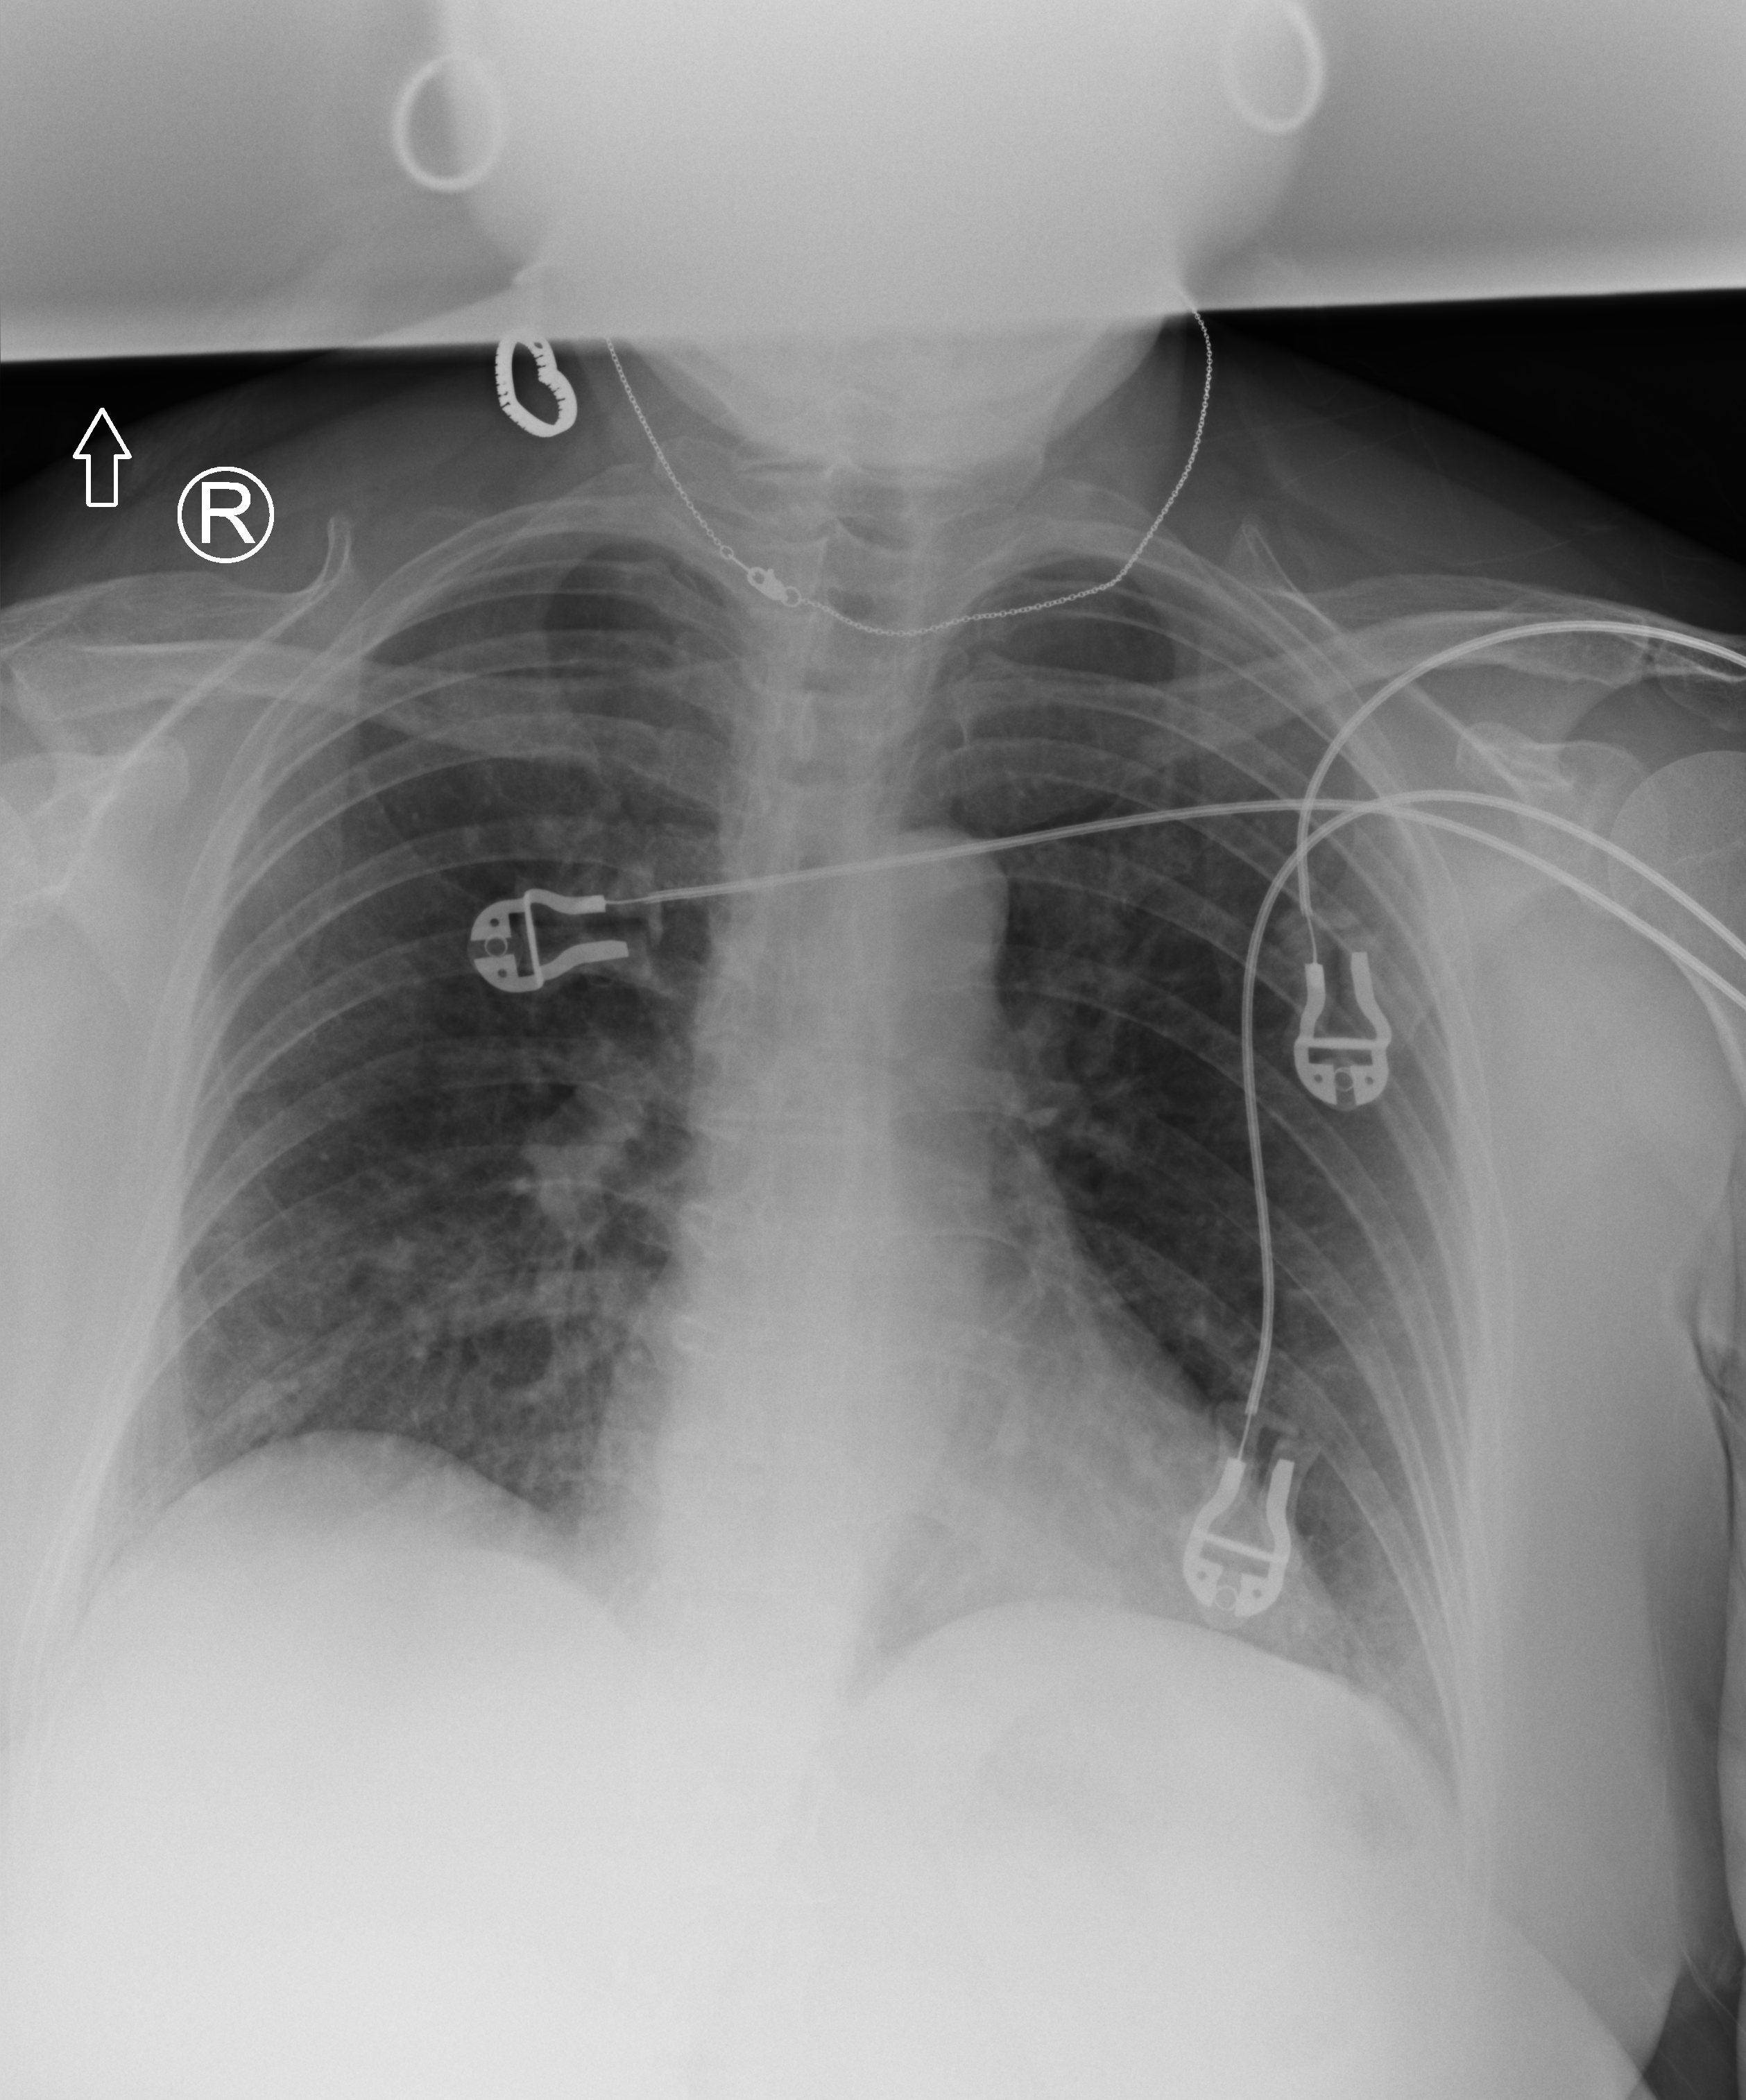
Chest X-ray (portable); anteroposterior (AP) projection. Patient hospitalised with COVID-19; female, aged 18–59 years.
Admission-level facts for this patient (not findings on this image; timing relative to this image not recorded): admitted to intensive care during this hospital stay: no; length of hospital stay: 3 days; mechanically ventilated during this hospital stay: no.